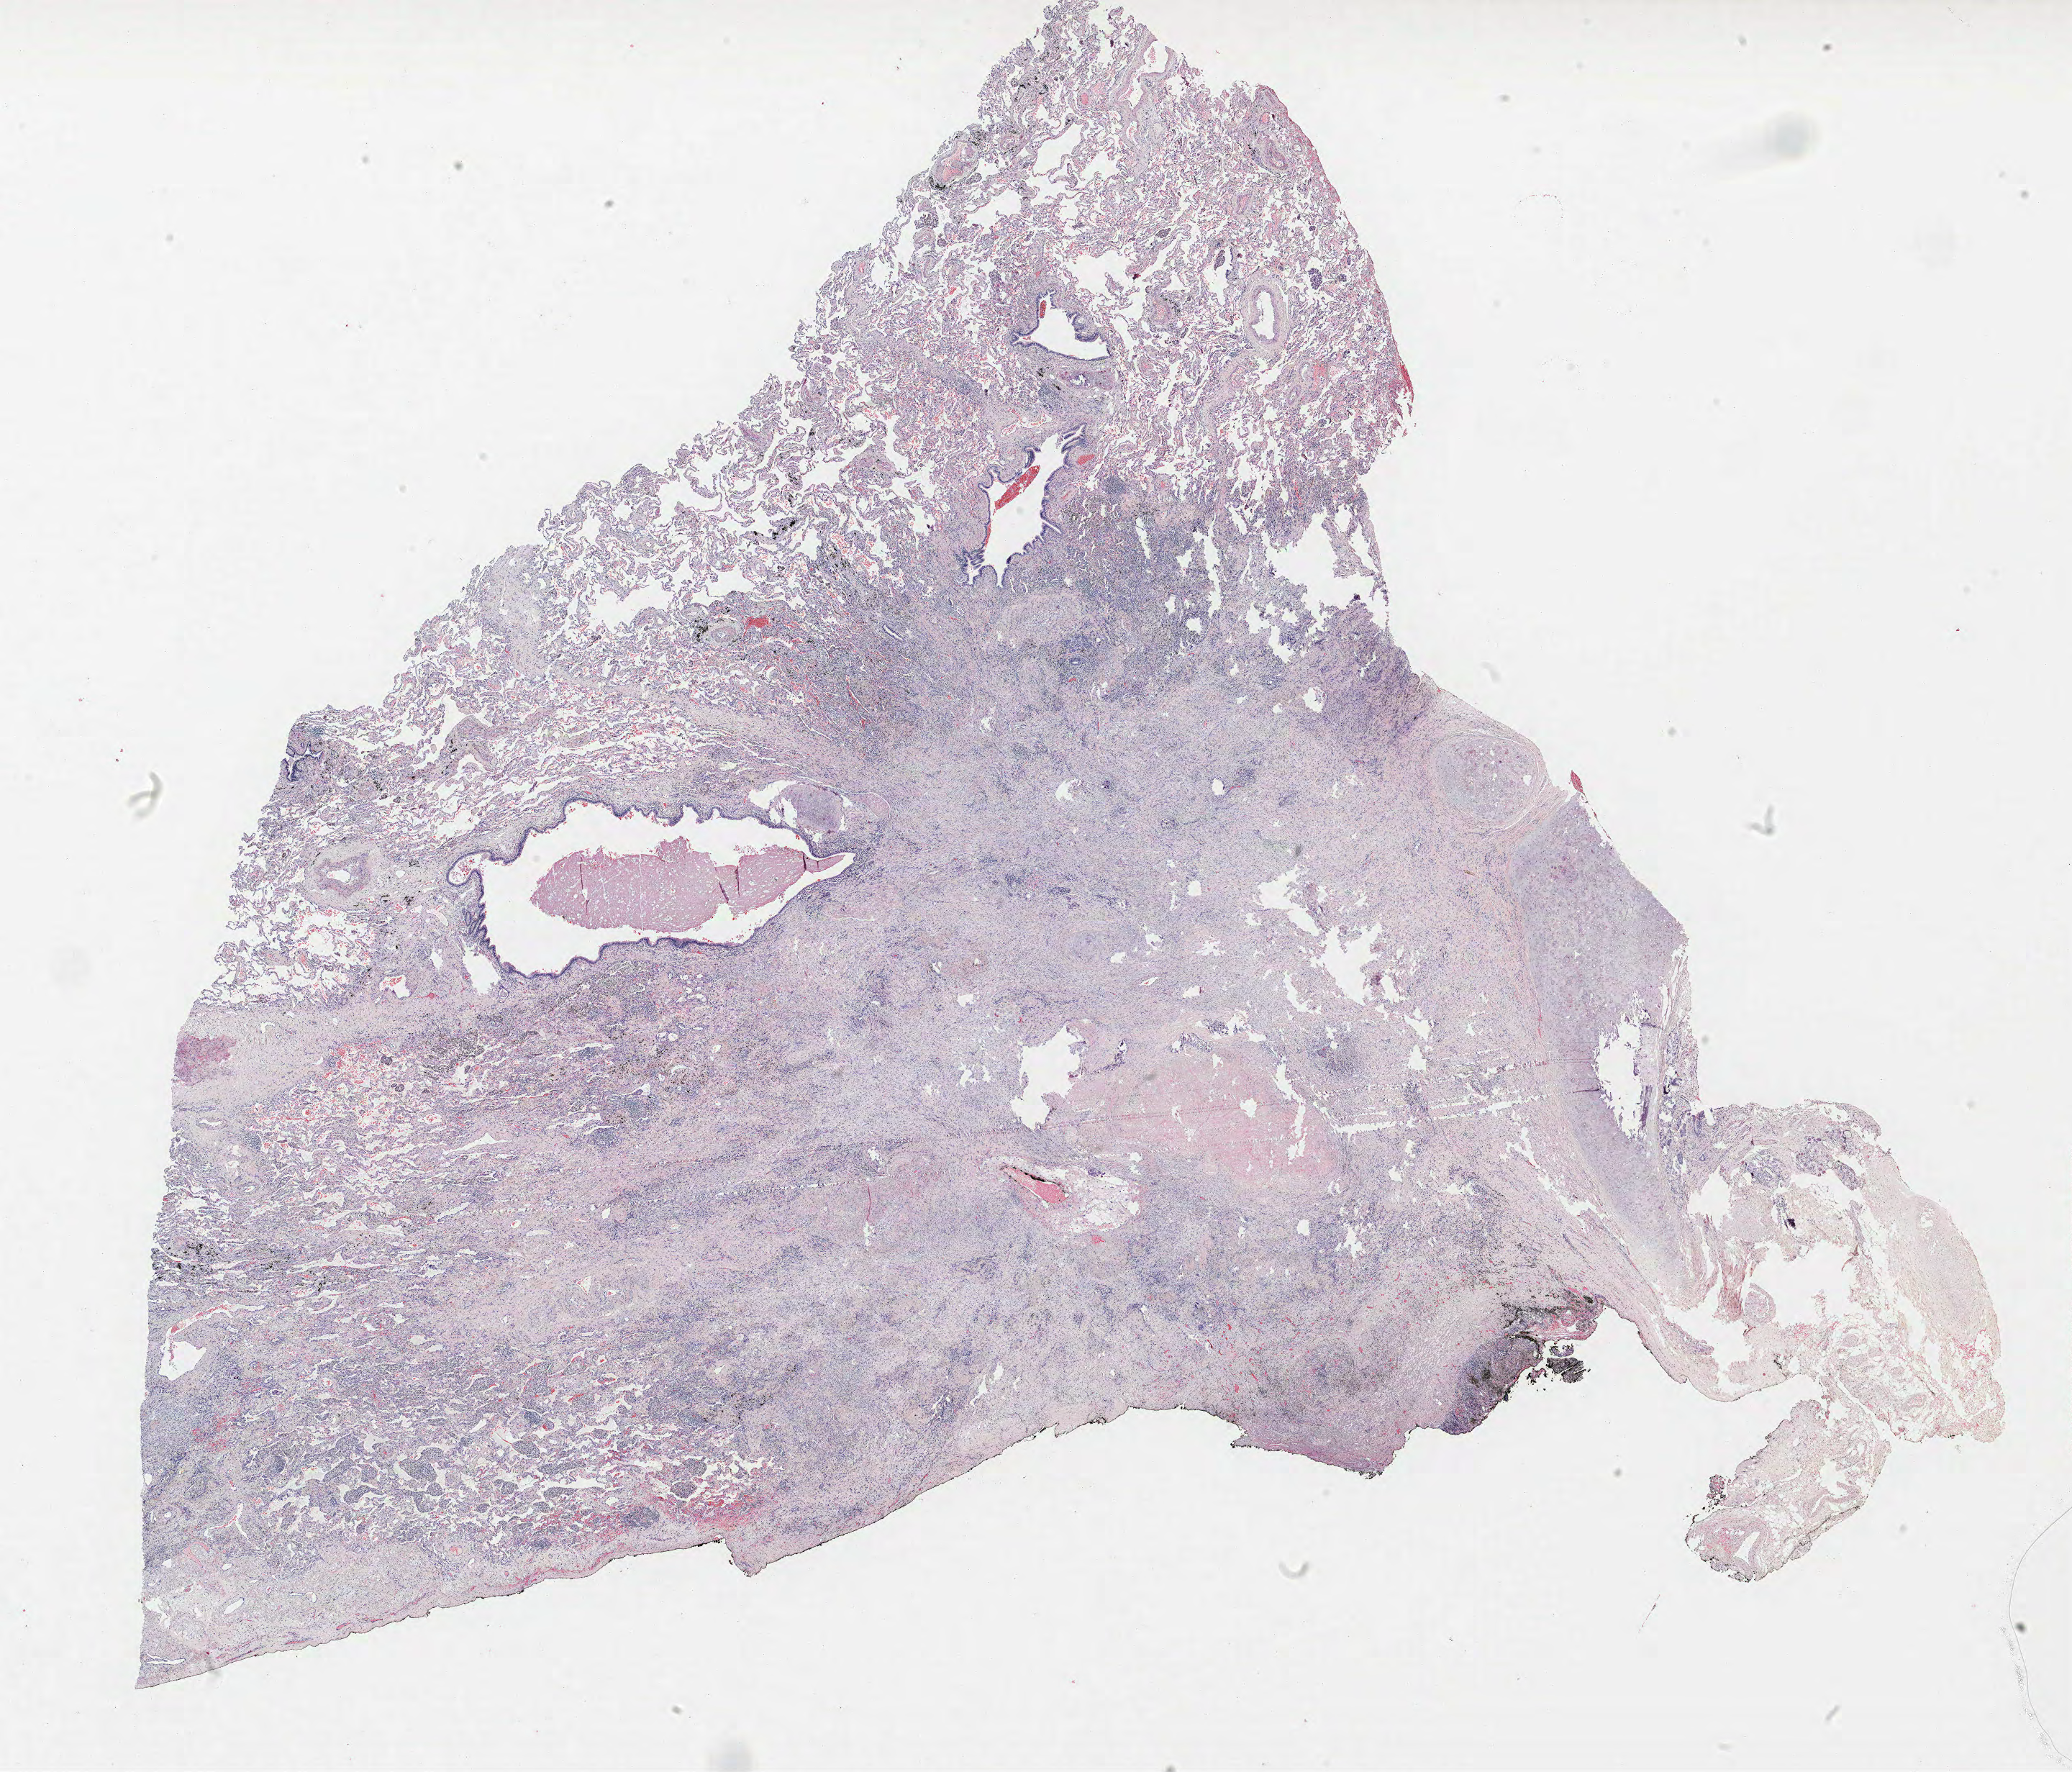
H&E whole-slide image — shown as a low-resolution overview of the whole scanned area (about 23.0 x 19.7 mm), FFPE section, lung tissue. Female, age 61 at enrolment.
Participant's lung-cancer diagnosis: Squamous cell carcinoma, NOS.